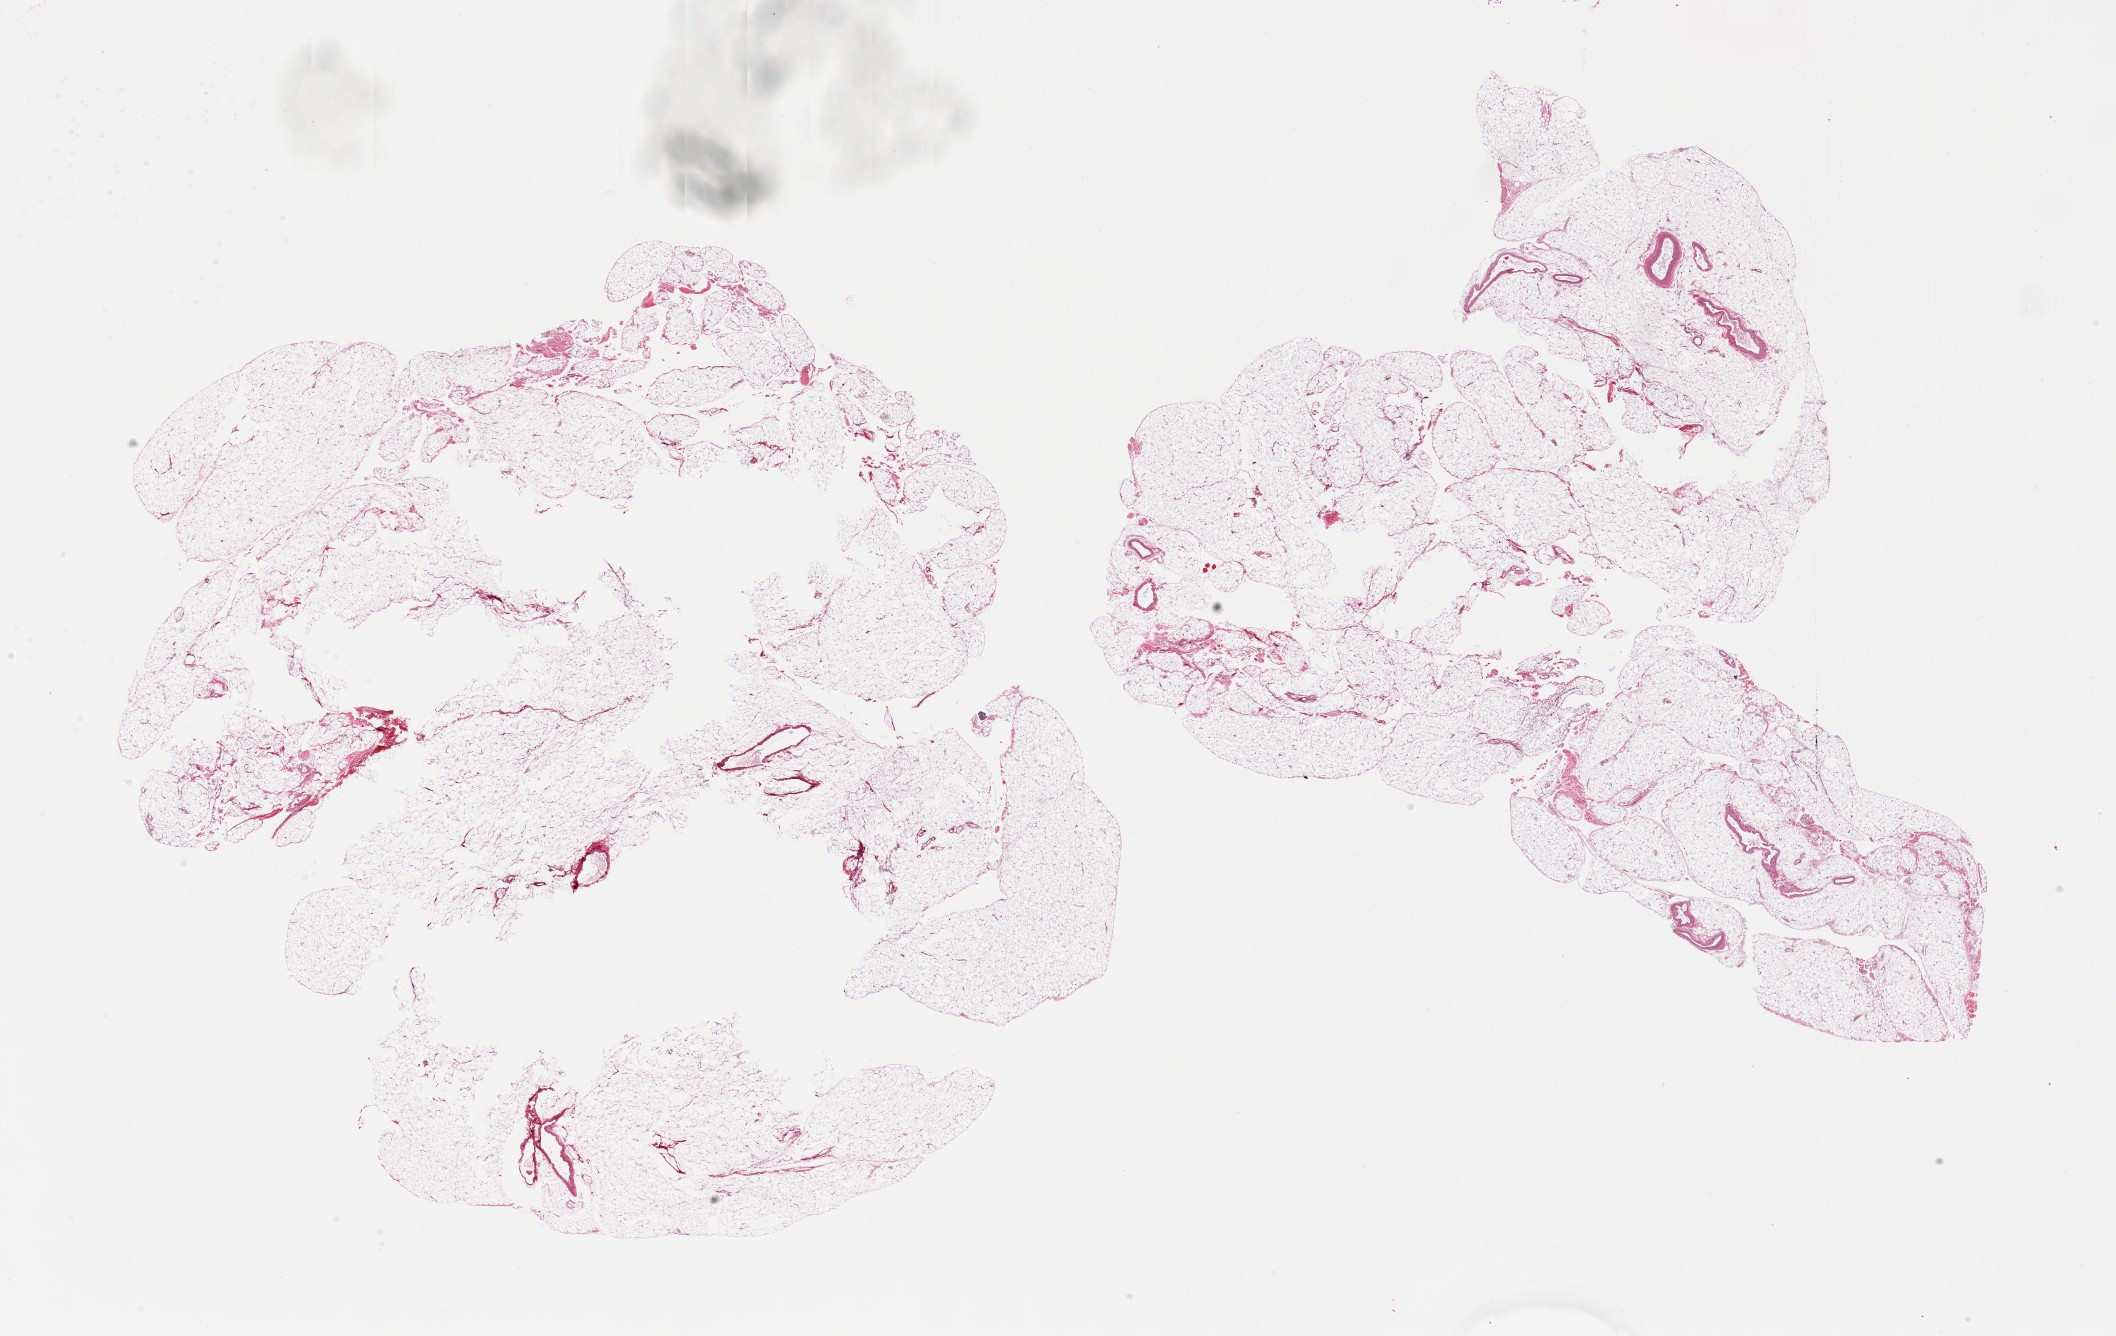
Digitized hematoxylin and eosin (H&E)-stained section — low-resolution overview of the scanned area, about 33.5 x 21.1 mm; PAXgene-fixed paraffin-embedded (PFPE) section; sampled site (target tissue): omentum; tissue donor sample. Male donor.
Pathologist's review note for this sample: 2 pieces; over-sized and with central defects (?poor fixation).